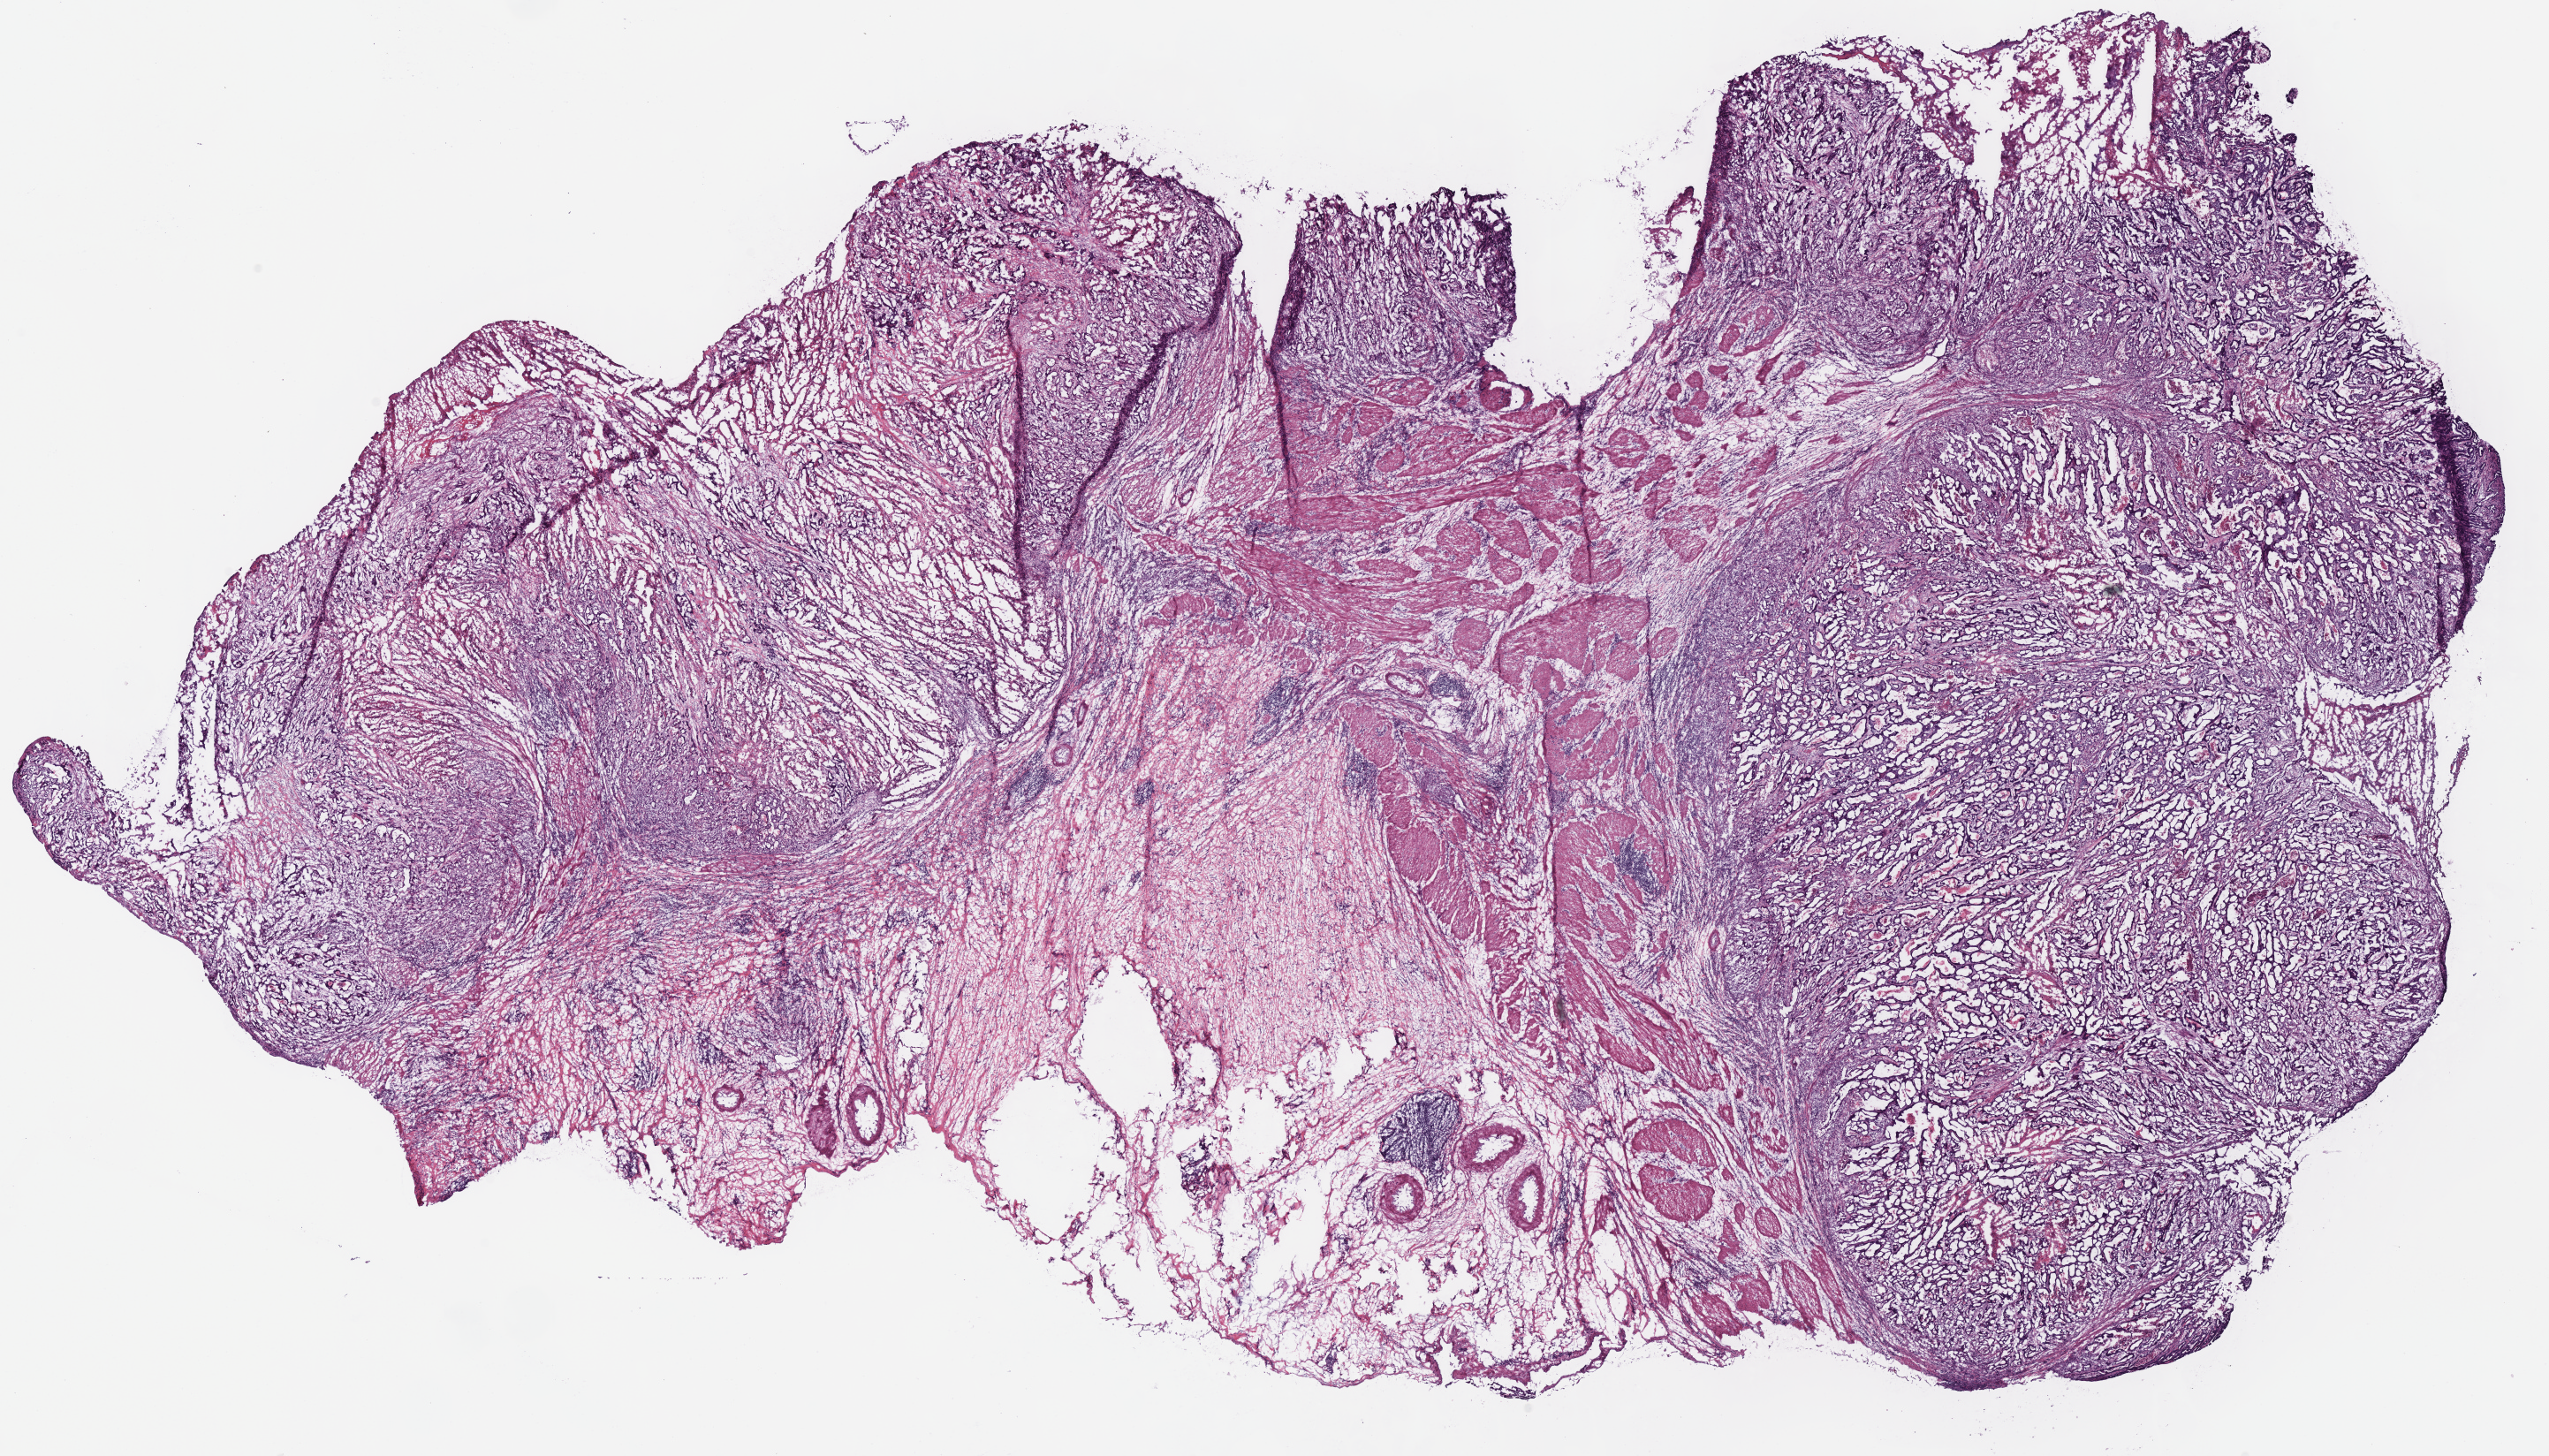
Whole-slide histology image, H&E, a low-resolution overview of the entire scanned area, about 22.7 x 13.0 mm (from a 40x scan), frozen section from the top of the tissue portion, sample: primary tumour, stomach. Male patient; age at initial diagnosis 74 years. Histologic grade: G3 (poorly differentiated). Pathologist review of this section (percent, as recorded): tumour cells 60%, tumour nuclei 60%, normal cells 0%, stromal cells 30%, necrosis 10%.
AJCC pathologic stage: IIB (7th edition). TNM: T4a N0 M0. Diagnosis: Adenocarcinoma, intestinal type (body of stomach).